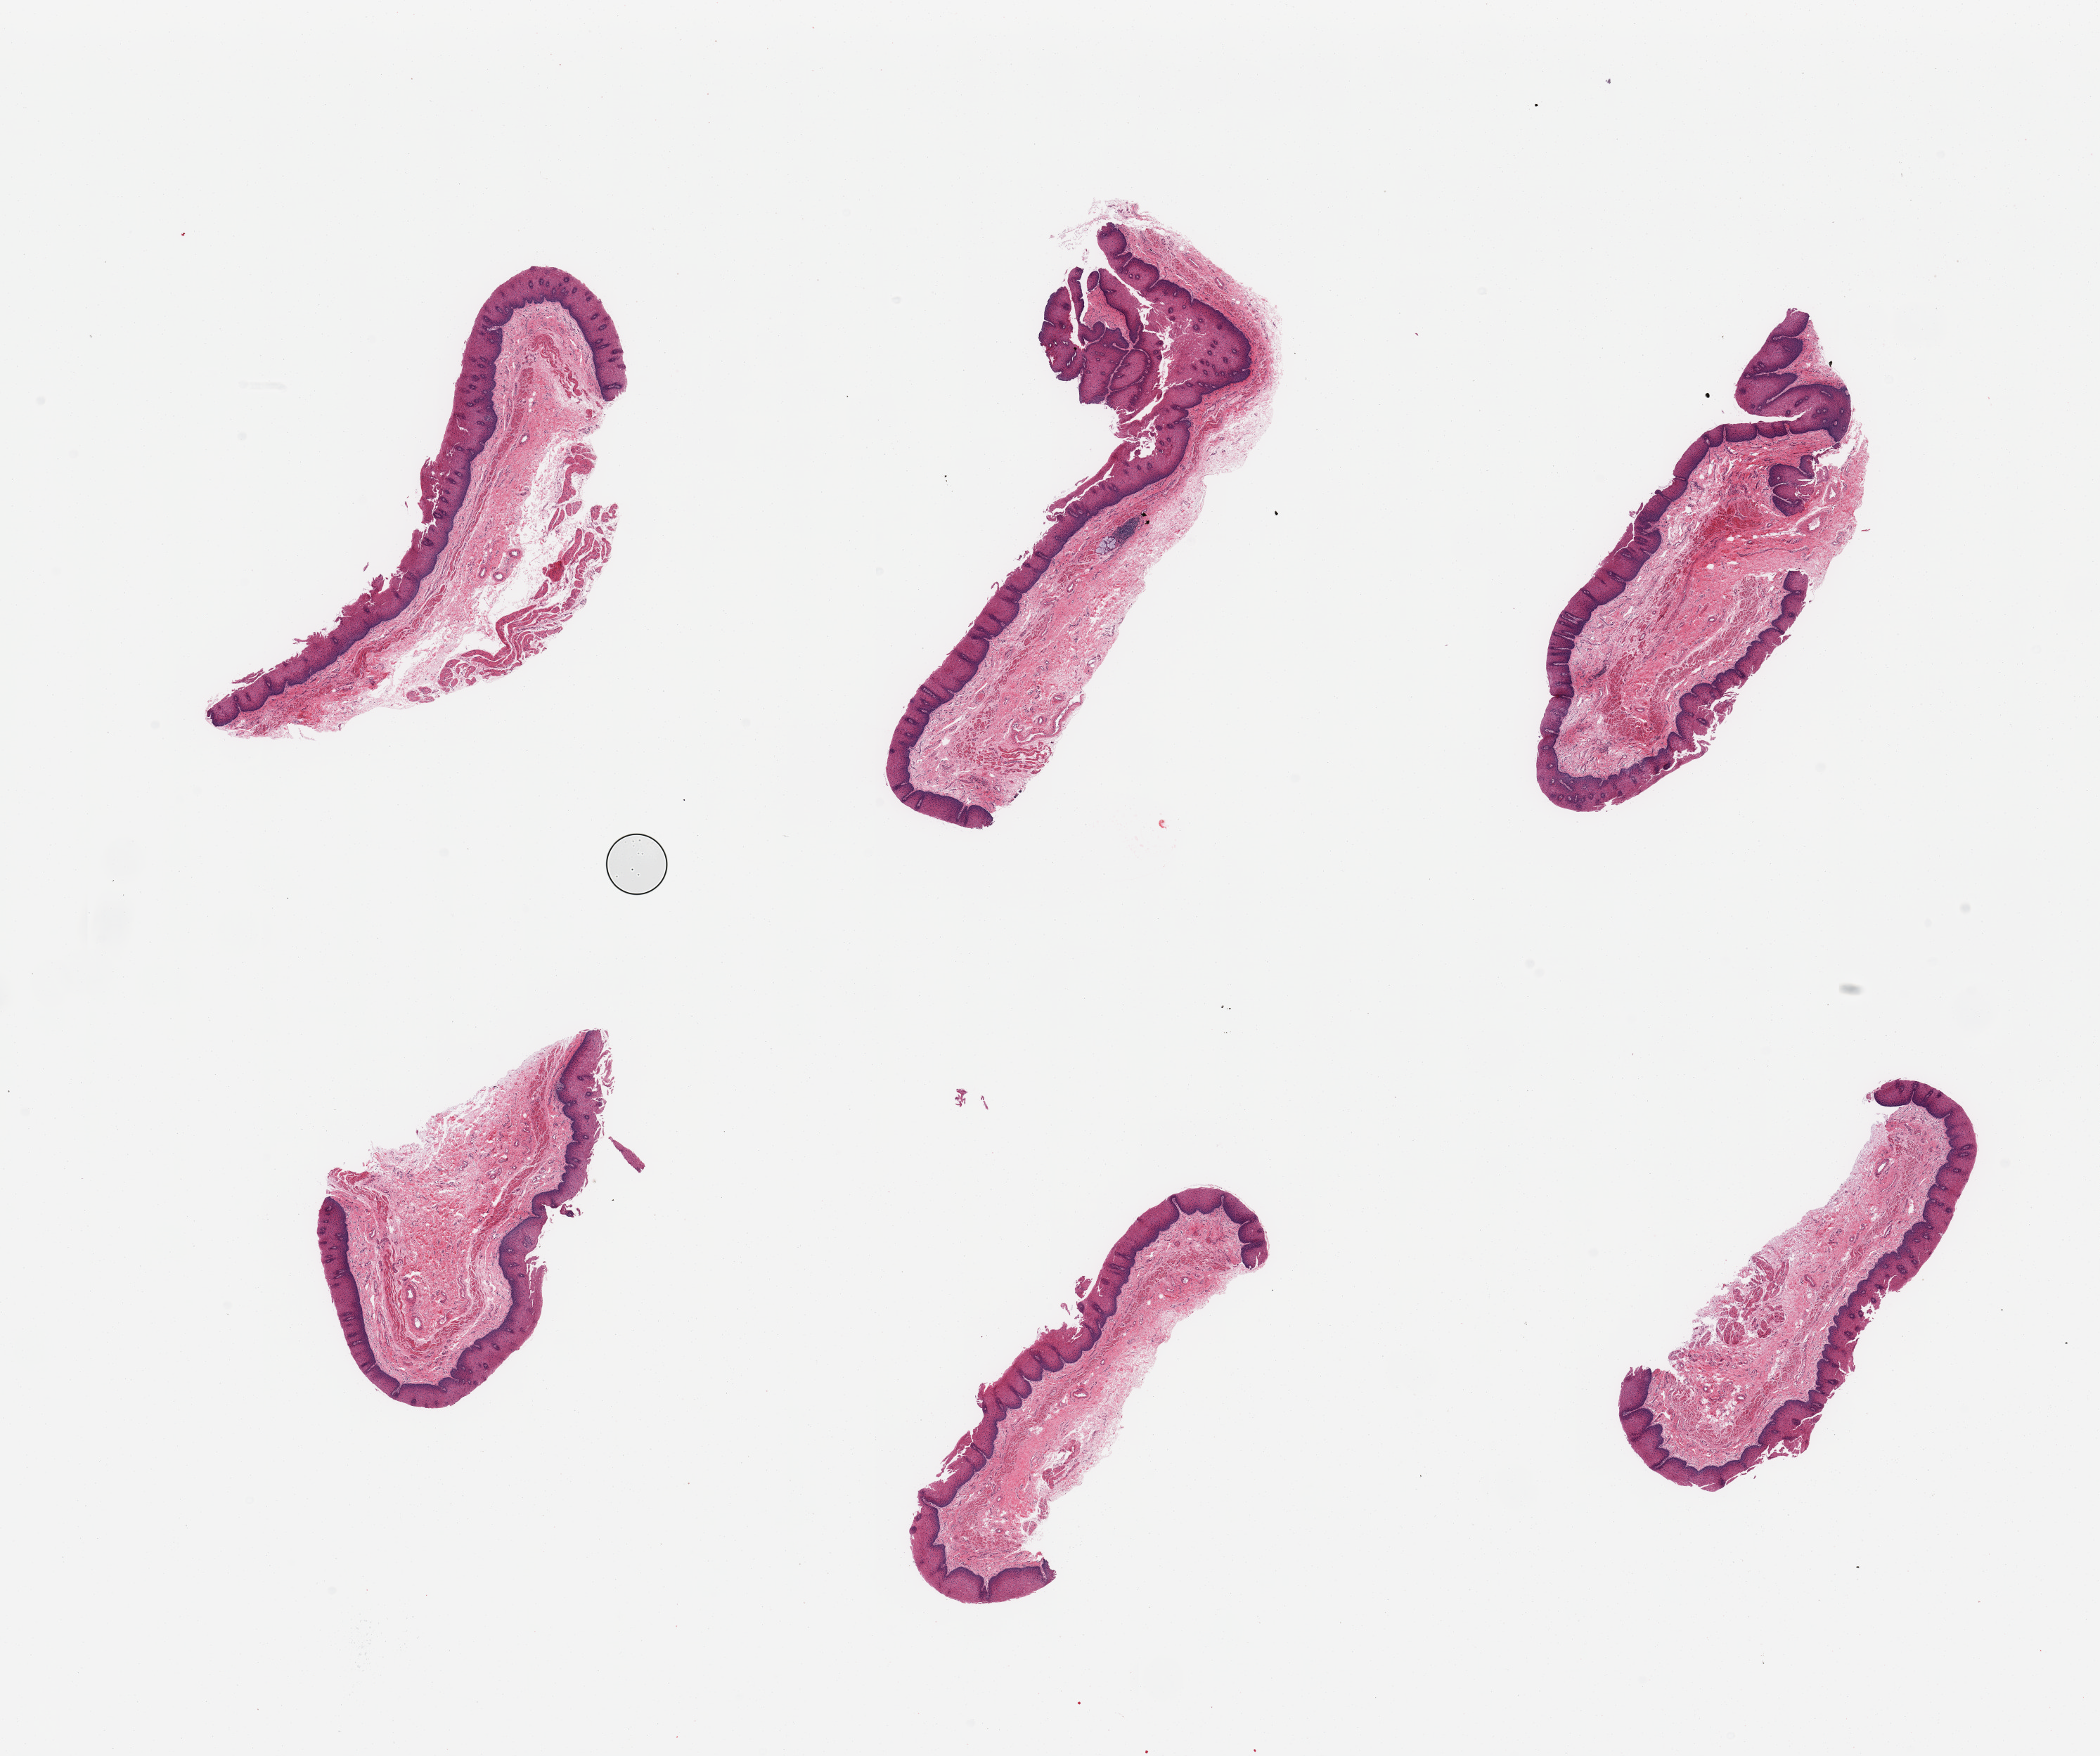
H&E whole-slide image, low-resolution overview of the scanned area, about 23.6 x 19.8 mm (acquisition: 20x scan), PAXgene-fixed, paraffin-embedded tissue, target tissue: esophageal mucous membrane, donor tissue sample. Donor sex: male.
Review note (as recorded): 6 pieces; few pieces include small portion of muscularis propria (not target).